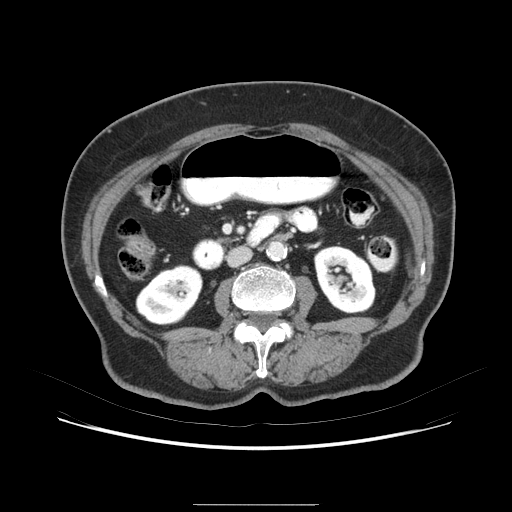
Contrast-enhanced abdominal CT (liver protocol), one axial slice. Position 15 of 79 along the scan axis. 120 kVp. Soft-tissue window (W 400 / L 40 HU). 2.5 mm slice thickness. 512 × 512 image matrix. Case-level facts recorded for this patient, not image findings: diagnosis: hepatocellular carcinoma (patient treated with transarterial chemoembolisation; whether this scan precedes or follows treatment is not stated here); TNM stage (as recorded): Stage-I; Child-Pugh class: A; tumour differentiation: poorly differentiated; tumour nodularity: uninodular.
Outlined on this slice (semi-automatically segmented with operator editing):
- liver parenchyma outside the tumour (the mass and vessels are separate outlines, so this box may not span the whole liver): bounding box <104,212,114,246> (left, top, right, bottom; pixels)